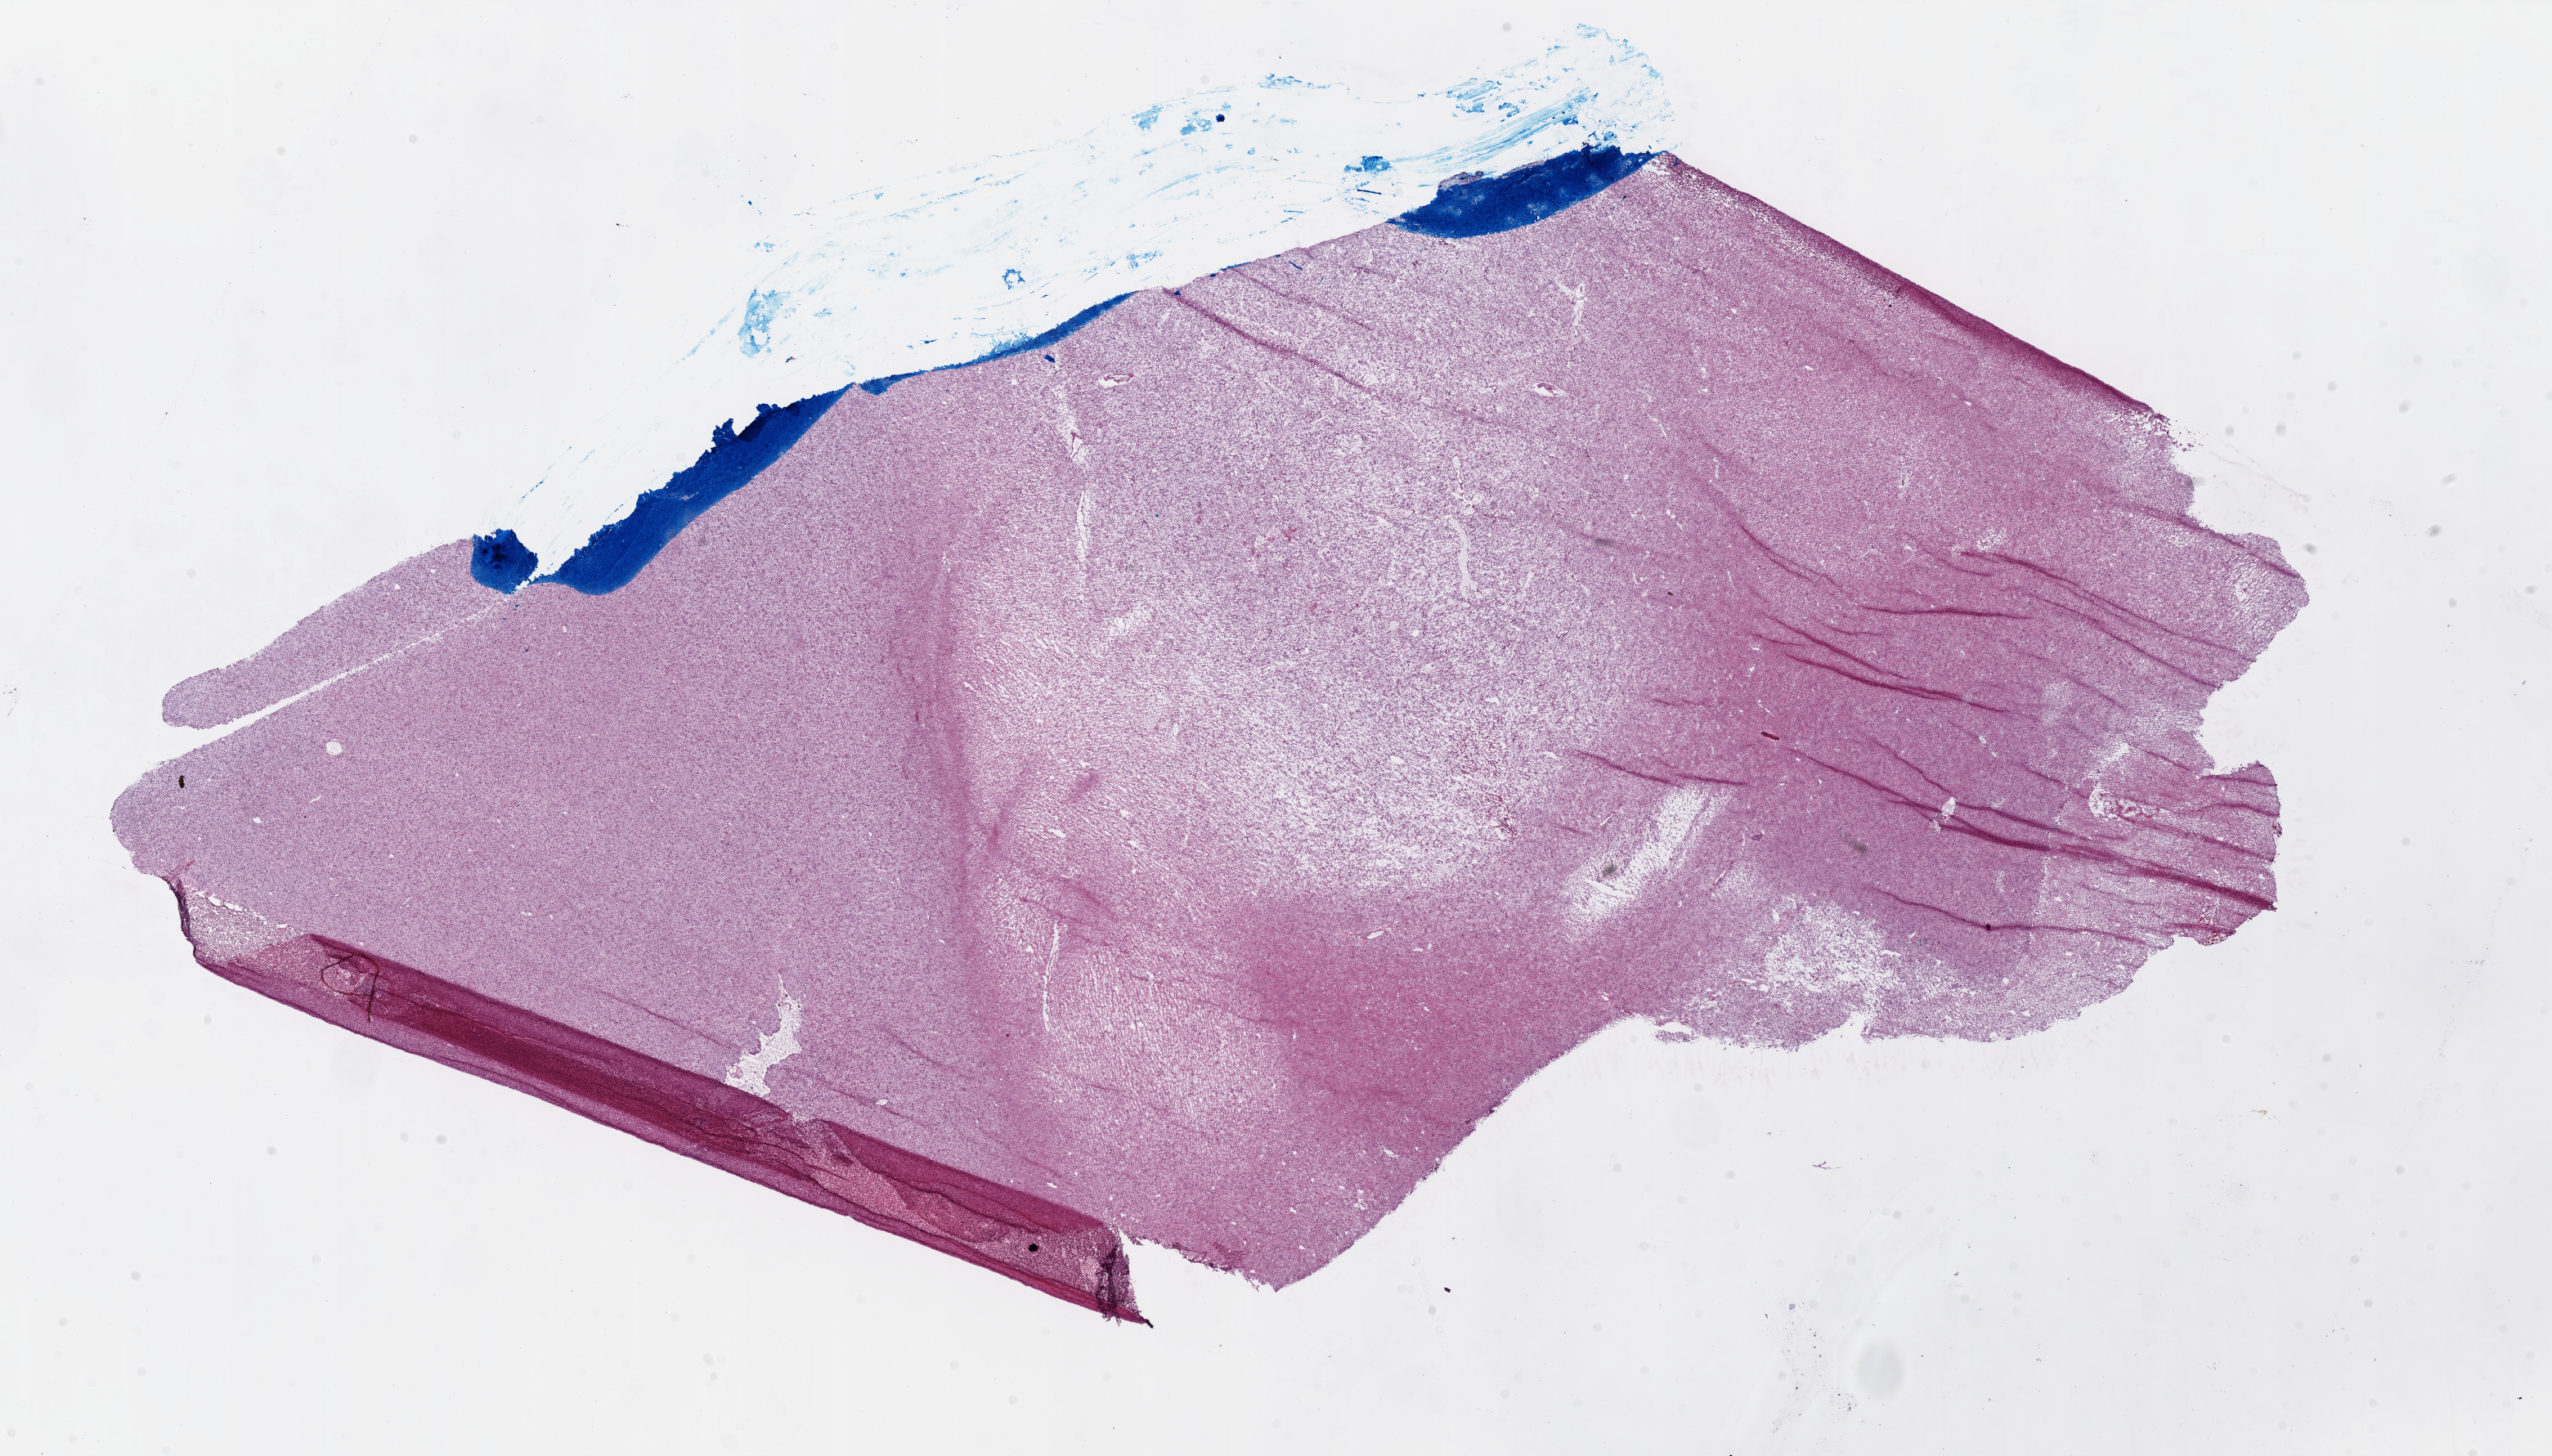
Digitized H&E tissue section (whole slide) — shown as a low-resolution overview of the whole scanned area (about 25.0 x 14.3 mm, slide scanned at 20x), frozen section from the top of the tissue portion, brain, primary tumour sample. Female patient; age at initial diagnosis 62 years. Pathologist review of this section (percent, as recorded): tumour cells 65%, tumour nuclei 90%, normal cells 0%, stromal cells 30%, necrosis 5%. Infiltration values recorded for this section: lymphocyte infiltration 0%.
* histologic diagnosis: Glioblastoma